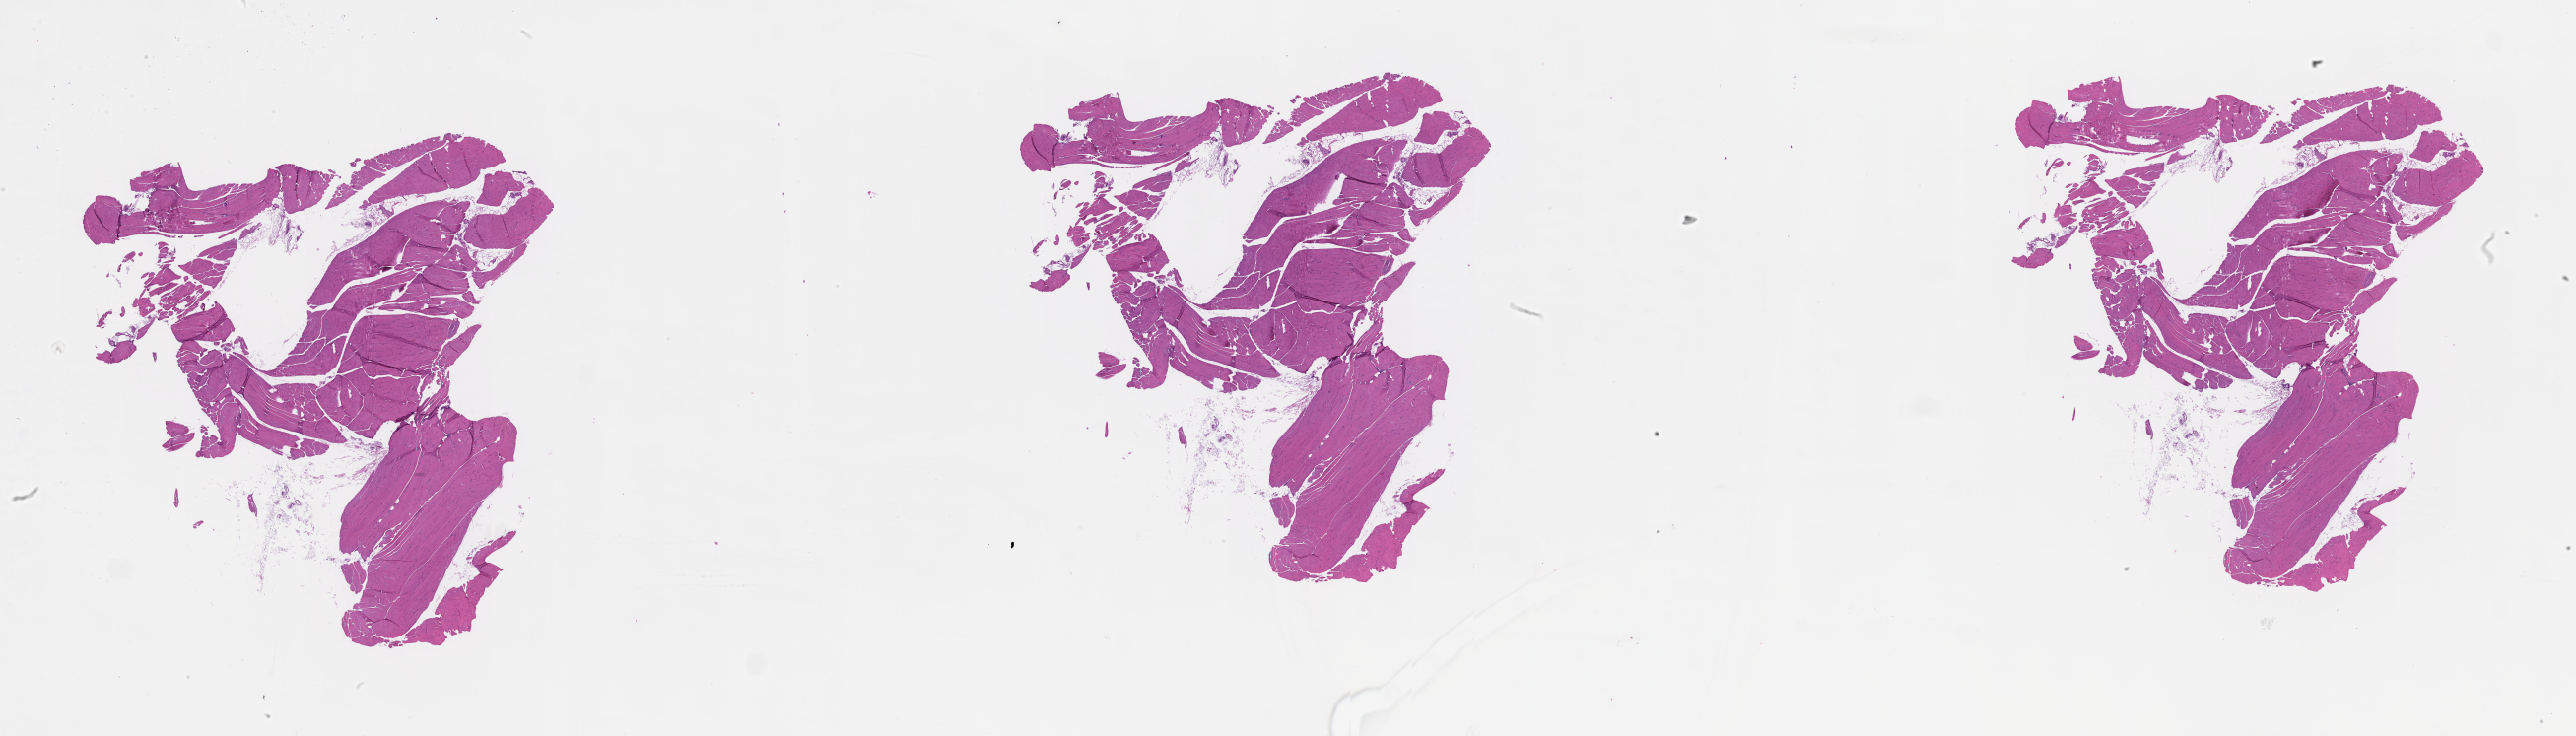
Digitized H&E tissue section (whole slide) — shown as a low-resolution overview of the whole scanned area (about 42.1 x 12.0 mm, slide scanned at 20x).
- patient diagnosis (cohort enrolment): sarcoma (site not recorded at cohort level)